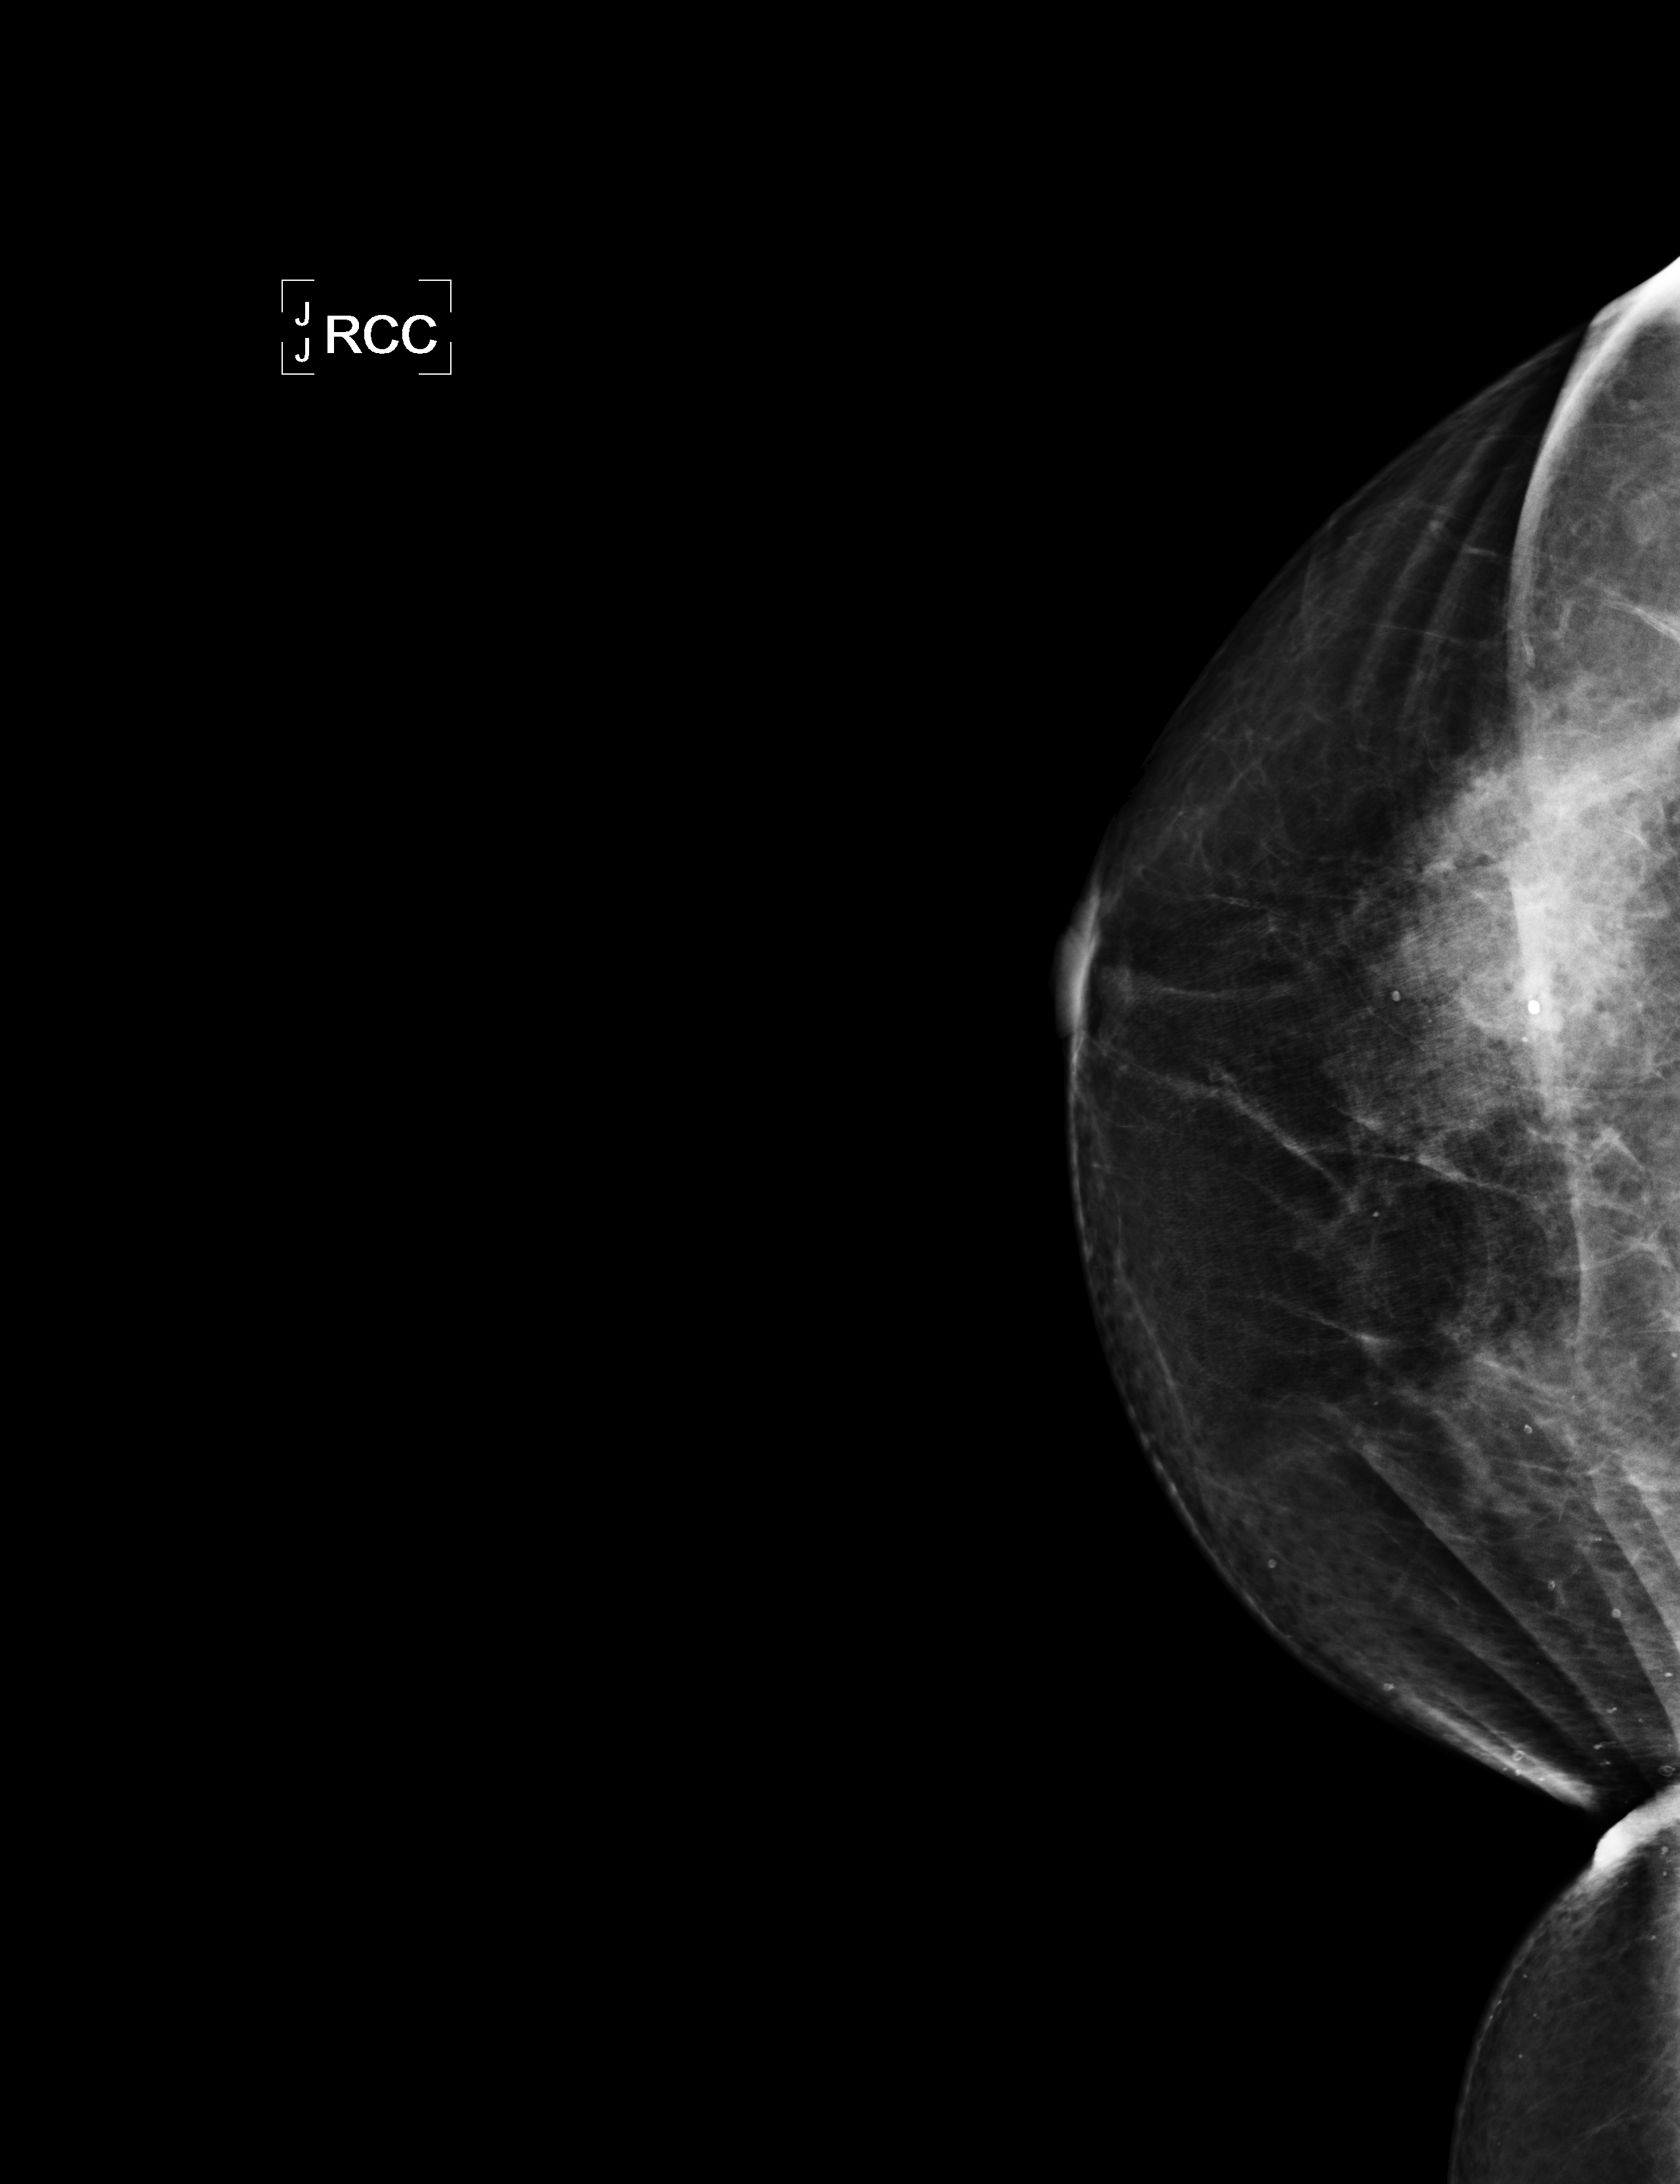
Diagnostic work-up study, system: Lorad Selenia. Patient: female, 68 years.
Image type: full-field digital mammogram. Breast: right. Projection: craniocaudal (CC) view.